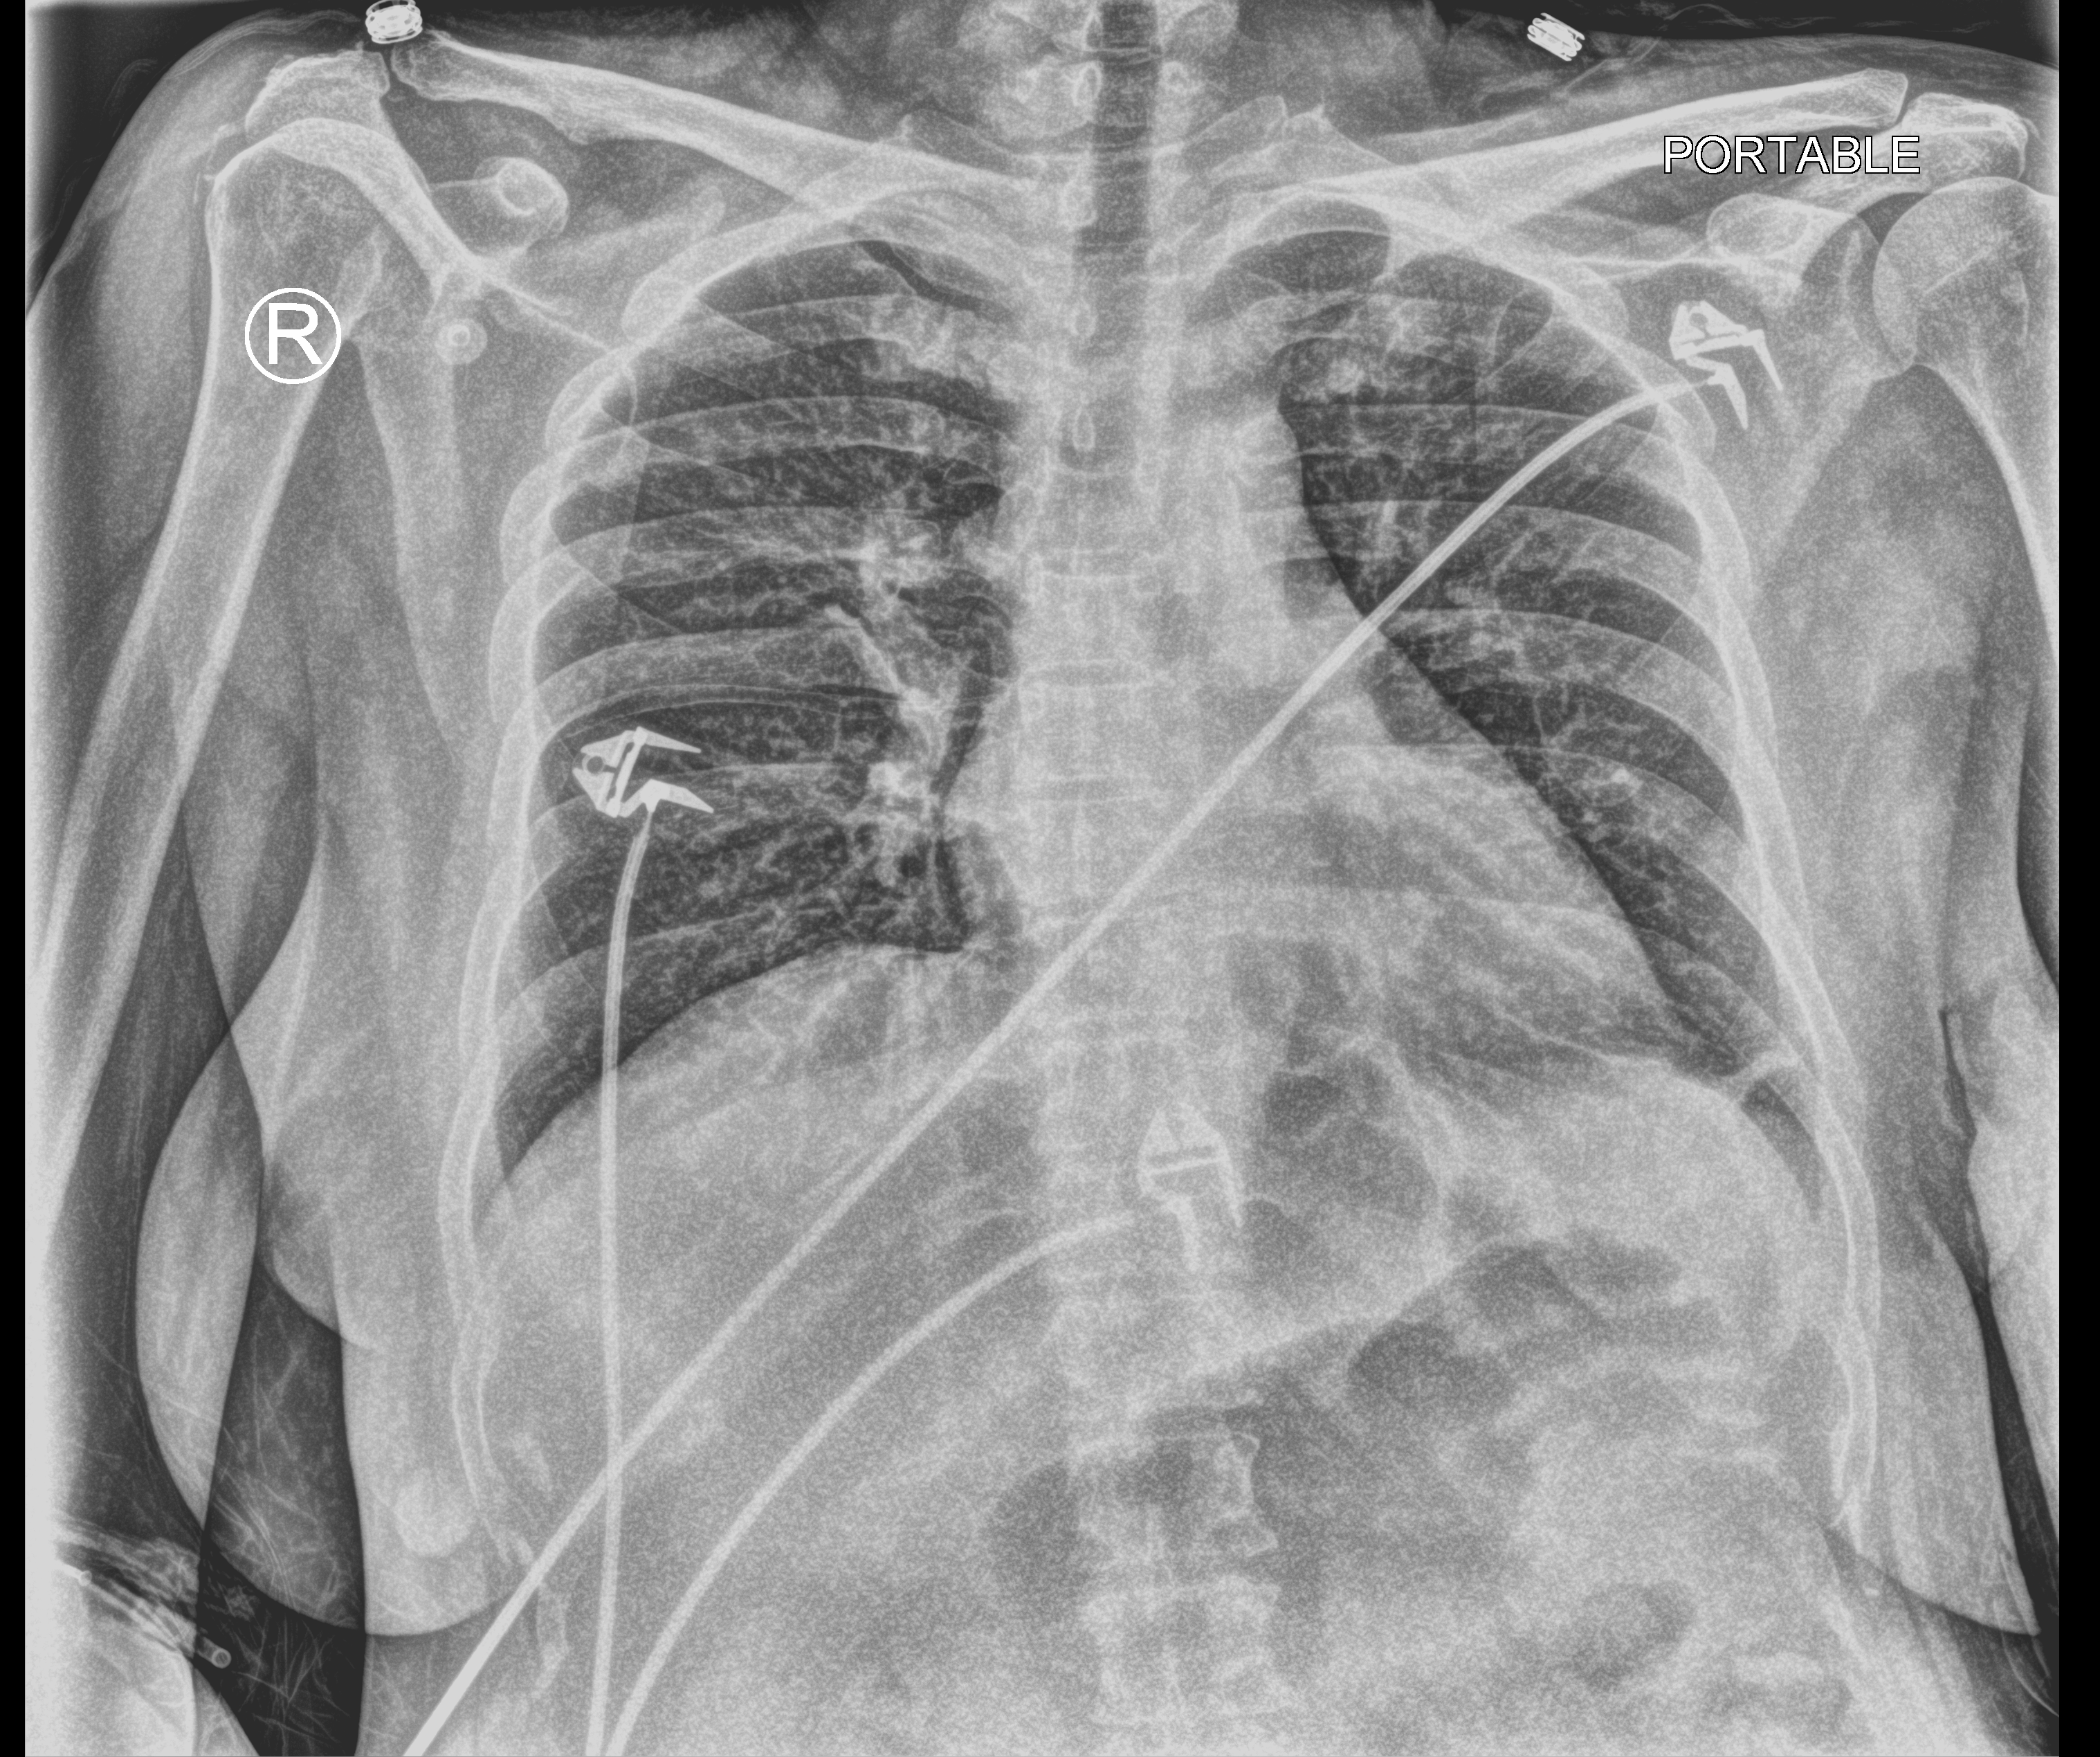
Chest X-ray (portable); anteroposterior (AP) projection. Female patient hospitalised with COVID-19, age 18–59 years.
Hospital-stay facts (about this admission, not read from this image; timing relative to this image not recorded):
- length of hospital stay: 10 days
- chronic kidney disease (admission record): yes
- other chronic lung disease (admission record): no